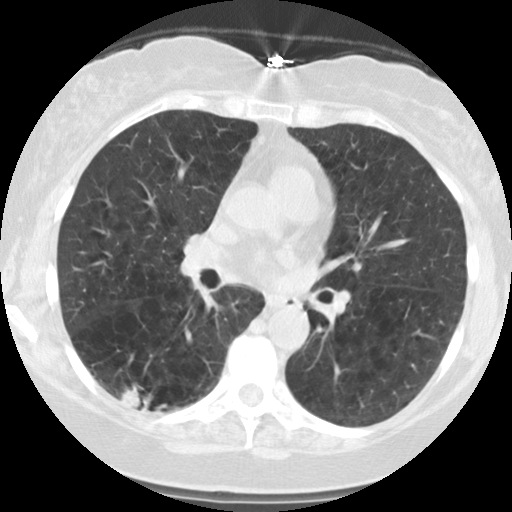
Low-dose screening chest CT, axial slice; second annual screen; lung window (W 1500 / L -600 HU); slice 62 of 122 in the series; 512 × 512 image matrix. Female participant, aged 59 years at enrolment. Current smoker at enrolment.
Expert-annotated lung lesion, box from (x=106, y=362) to (x=182, y=424) px. The screening reader recorded 2 non-calcified nodules or masses ≥4 mm on this exam (right lower lobe, right lower lobe); which of them this box marks is not recorded.